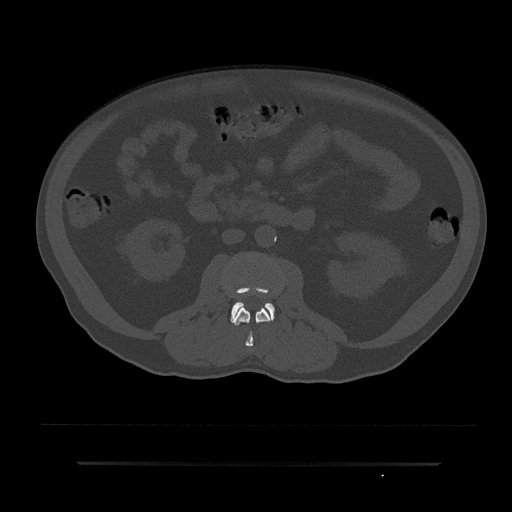
CT including the spine, one axial slice; reconstruction kernel Br40s/3; 120 kVp; bone window (W 1800 / L 400 HU); 0.5 mm slice thickness; 512 × 512 image matrix, field of view 464 × 464 mm. Male patient, age 59 years. Case-level facts recorded for this patient, not image findings: primary cancer: bile ducts.
Annotated regions visible in this slice (semi-automatic segmentation, software-assisted and operator-edited):
- L2 vertebra: bounding box (x1, y1, x2, y2) in pixels: (233, 306, 272, 347)
- L3 vertebra: (231, 289, 275, 324)